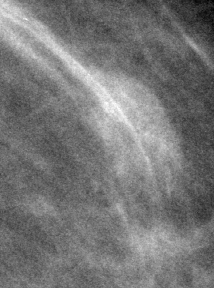
Region of interest cut from a scanned film mammogram (one marked finding); left breast; MLO view.
Finding: mass, shape oval, margins circumscribed; BI-RADS assessment category 4; pathology result (as recorded, not read from the image): malignant.